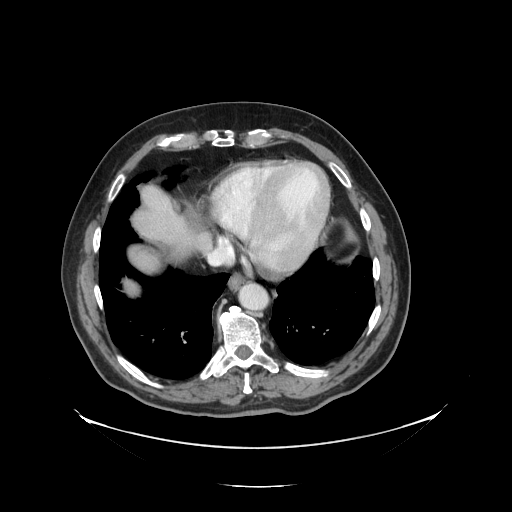
Contrast-enhanced abdominal CT, one axial slice; slice 122 of 138 in the series (ordered by position); reconstruction kernel STANDARD; intravenous contrast given; soft-tissue window (W 400 / L 40 HU); 2.5 mm slice thickness; 512 × 512 image matrix, field of view 497 × 497 mm. Male patient, age 77 years. From the clinical record (not read from this slice): diagnosis: colorectal cancer liver metastases, imaged before liver resection; multiple liver metastases: no; largest metastasis: 1.5 cm.
Structures marked on this image (expert manual segmentation):
- liver: bounding box <126,187,193,293> (left, top, right, bottom; pixels)
- planned liver remnant (the part of the liver to remain after resection): <130,187,193,272>